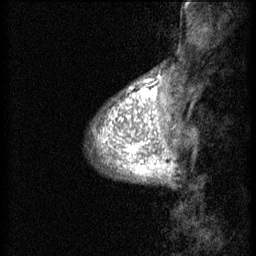
Breast MRI (dynamic contrast-enhanced), one sagittal slice. Position 10 of 60 along the scan axis. 3 images stored at this slice position (order not interpretable as contrast timing). 1.5 T. TE 4.2 ms, TR 8.2 ms. 2 mm slice thickness. 256 × 256 image matrix, field of view 180 × 180 mm. Female patient, age 38 years.
Annotated regions visible in this slice (semi-automatic segmentation, software-assisted and operator-edited):
- analysis volume of interest (the breast-tissue region the enhancement analysis was run in; not a lesion): bounding box <95,106,157,171> (left, top, right, bottom; pixels)
- tumour enhancement mask (voxels above the 70 % enhancement threshold inside the analysis volume of interest): <95,106,157,171>